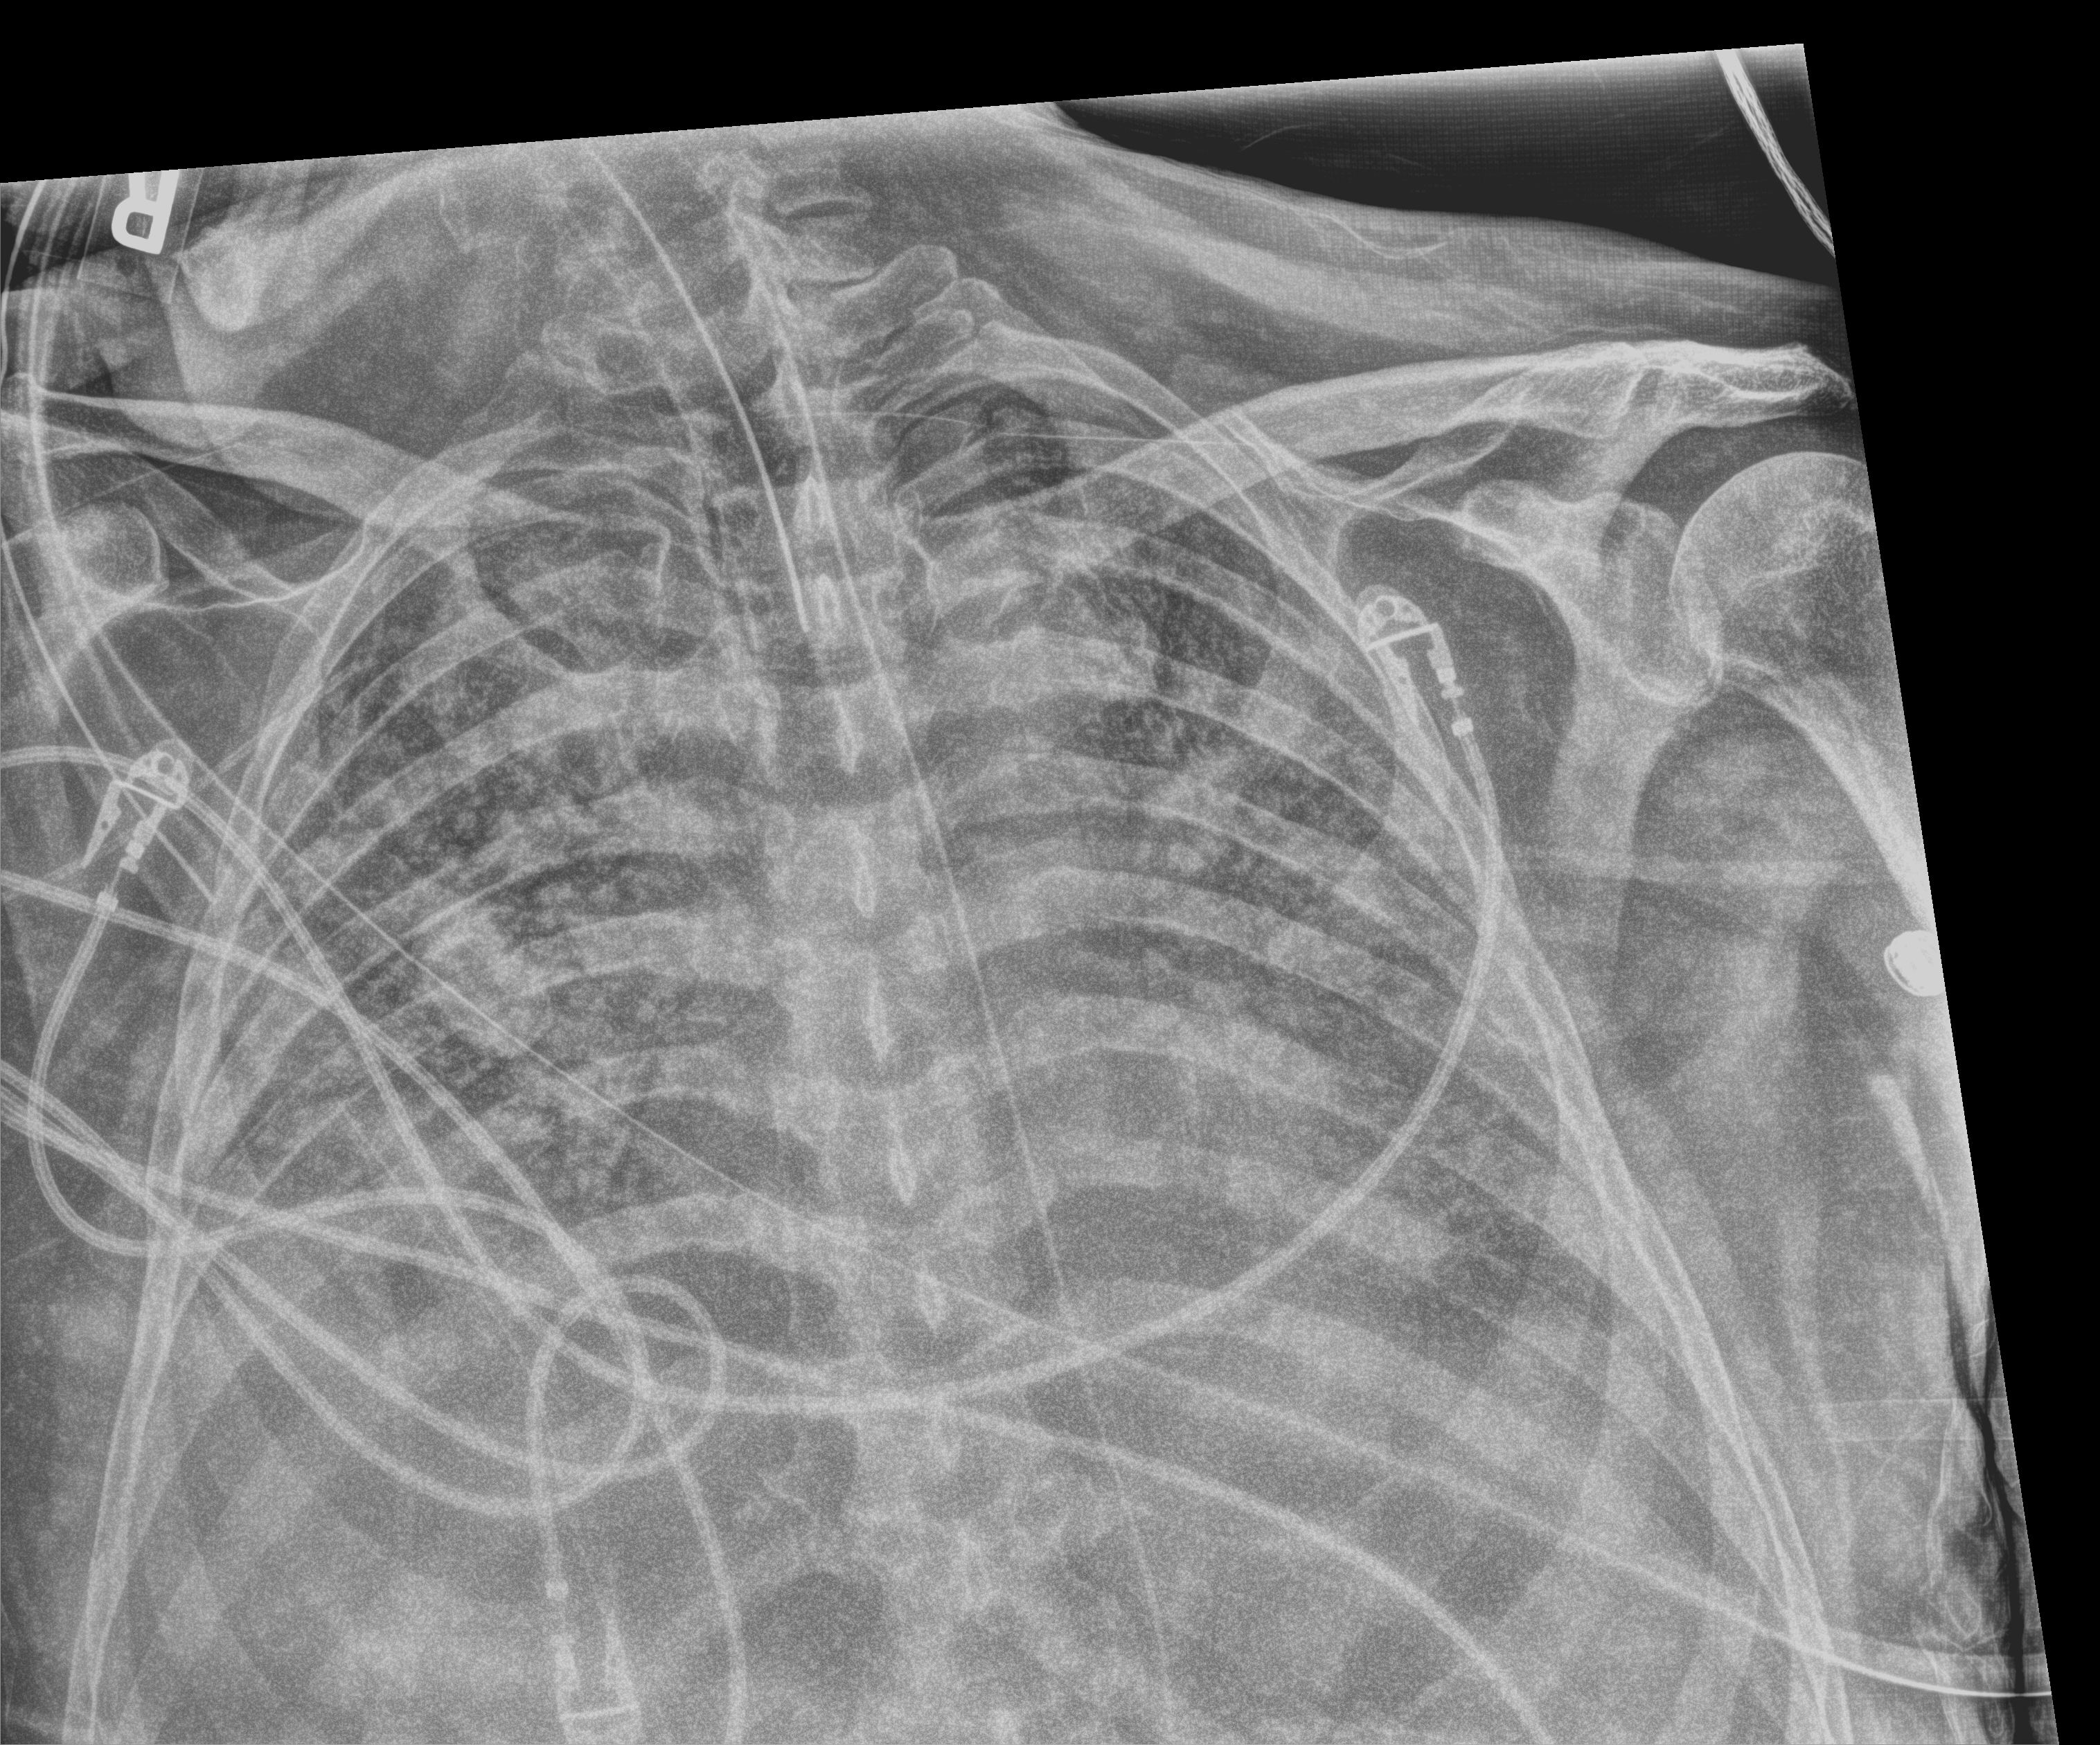
Chest X-ray (portable); anteroposterior (AP) projection. Patient hospitalised with COVID-19; male, aged 60–74 years.
Hospital-stay facts (about this admission, not read from this image; timing relative to this image not recorded): admitted to intensive care during this hospital stay: yes; length of hospital stay: 26 days.